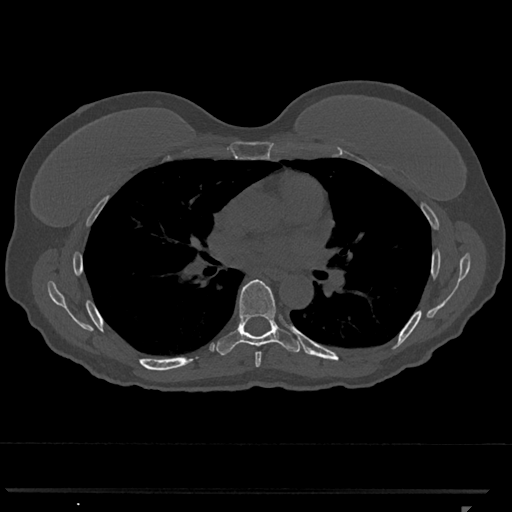
CT including the spine, one axial slice. Reconstruction kernel Br40s/3. 120 kVp. Bone window (W 1800 / L 400 HU). 512 × 512 image matrix, field of view 380 × 380 mm. Patient: female, 62 years. Case-level facts recorded for this patient, not image findings: primary cancer: renal.
Annotated regions visible in this slice (semi-automatic segmentation, software-assisted and operator-edited):
- T6 vertebra: box from (x=255, y=351) to (x=262, y=367) px
- T7 vertebra: (x=216, y=279)–(x=302, y=355)